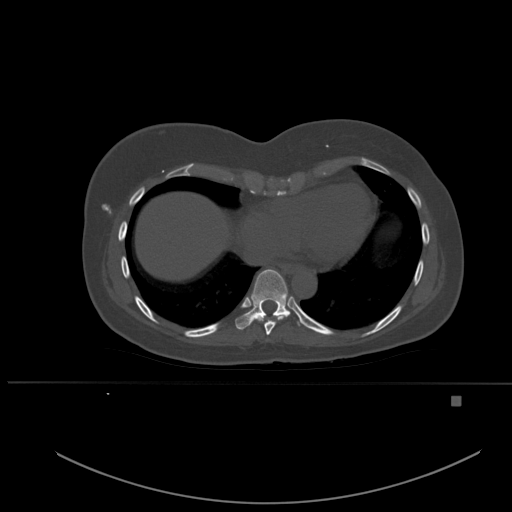
CT including the spine, one axial slice. Bone window (W 1800 / L 400 HU). 1.5 mm slice thickness. 512 × 512 image matrix, field of view 443 × 443 mm. Patient: female, 49 years. From the clinical record (not read from this slice): primary cancer: breast.
Structures marked on this image (semi-automatically segmented with operator editing):
- T8 vertebra: bounding box (x1, y1, x2, y2) in pixels: (257, 316, 288, 335)
- T9 vertebra: (235, 269, 301, 330)